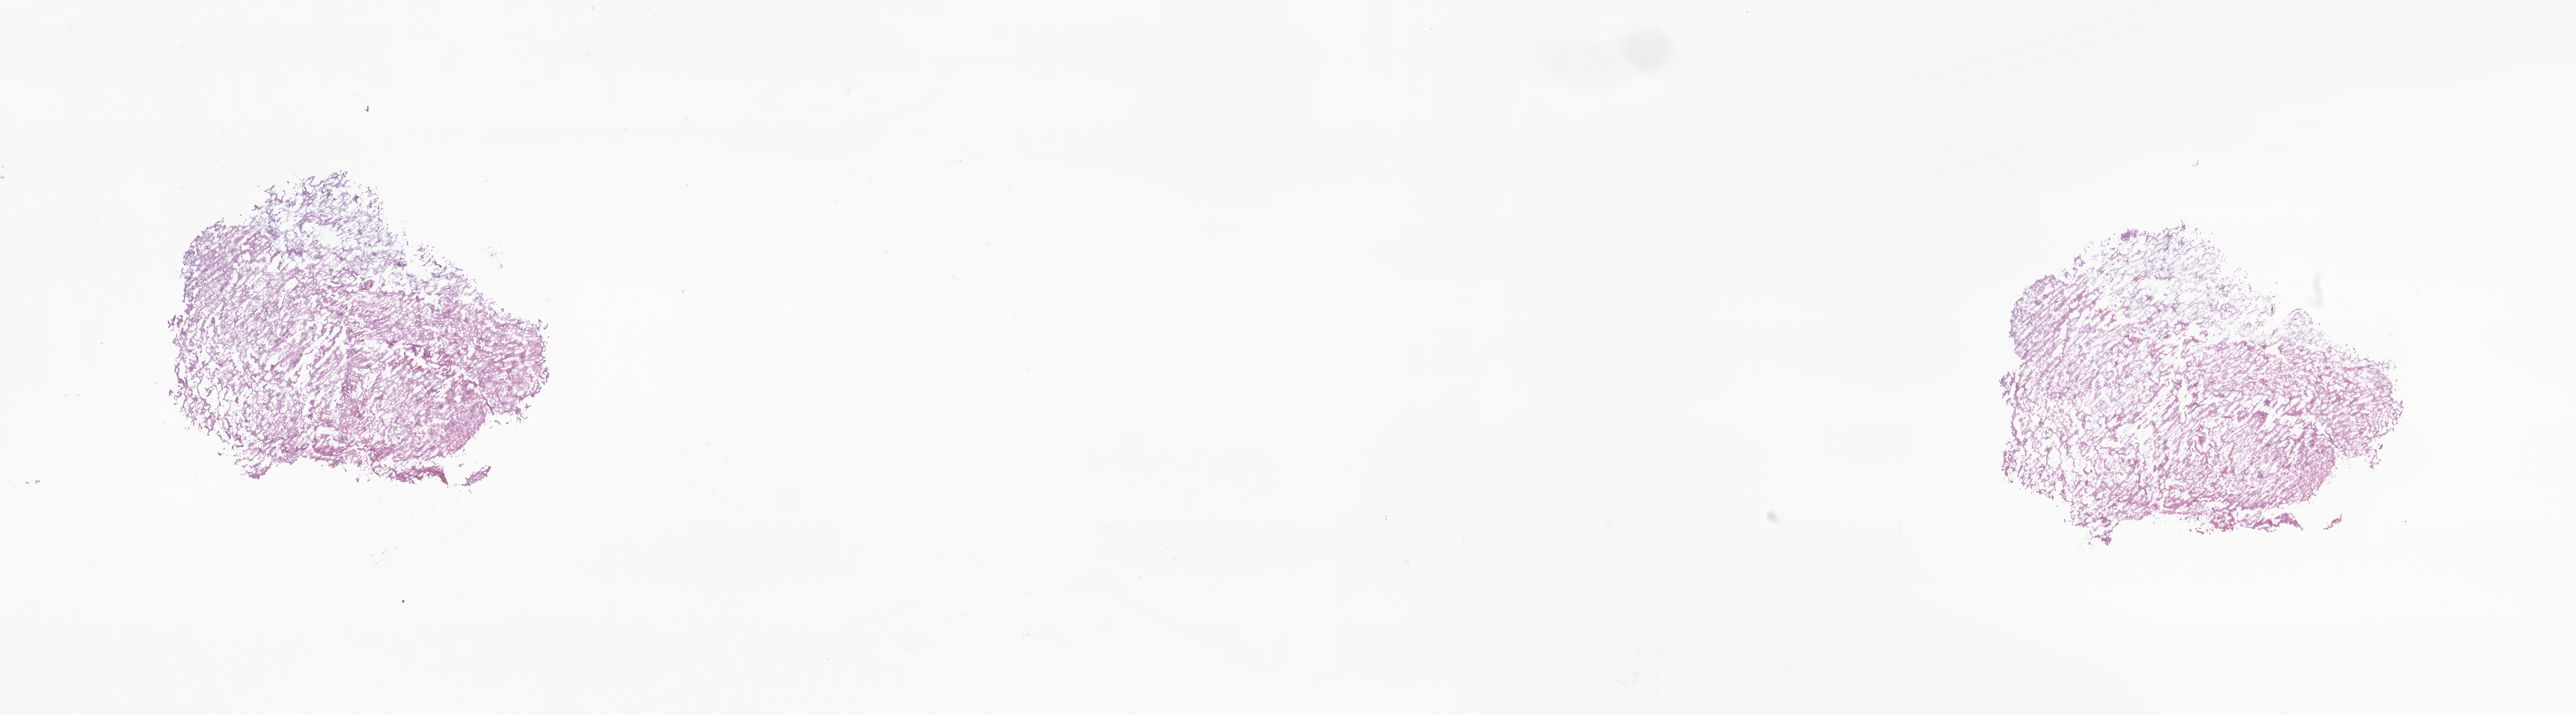
Whole-slide image, H&E stain of tumor tissue from the cerebellum, whole scanned area (about 27.7 x 7.7 mm) shown as a low-resolution overview. Cryosection (OCT / tissue freezing medium). Male patient, age 98 months.
Diagnosis: Pilocytic astrocytoma.